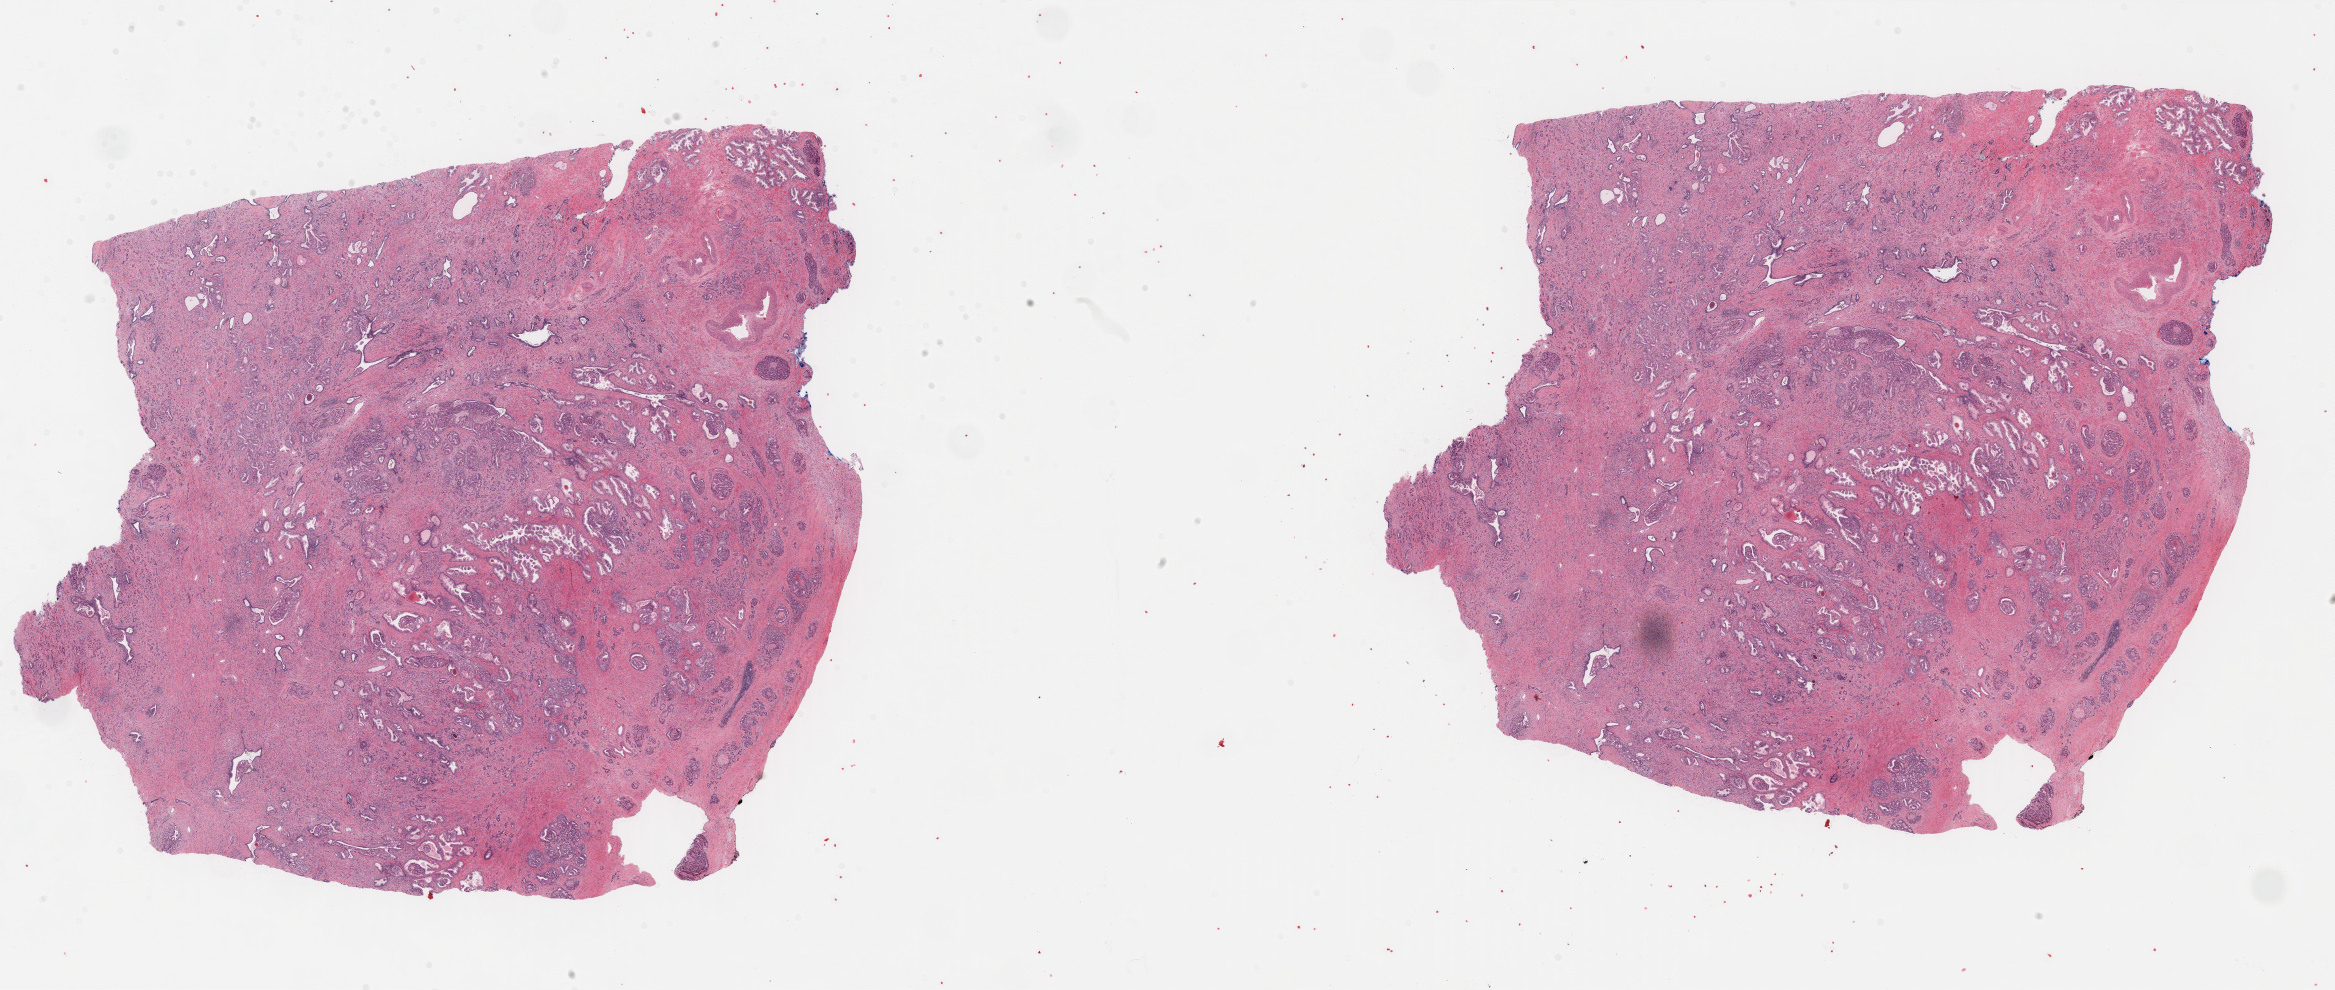
H&E-stained whole-slide image, shown as a low-resolution overview of the whole scanned area (about 36.9 x 15.7 mm, from a 40x scan); formalin-fixed paraffin-embedded (FFPE) diagnostic section; primary tumour sample from the prostate. Male patient; age at initial diagnosis 54 years. Gleason score: 7 (4+3).
Laterality: bilateral. Histologic diagnosis: Adenocarcinoma, NOS (prostate gland). Lymph nodes positive (case pathology): 1 of 17 examined.